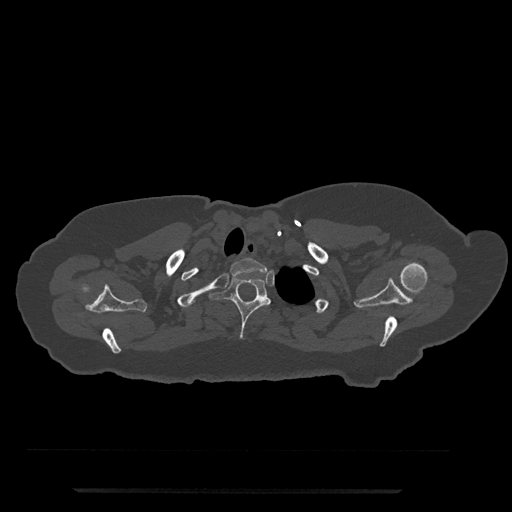
CT including the spine, one axial slice; slice 679 of 797 in the series (ordered by position); reconstruction kernel Br40s/3; bone window (W 1800 / L 400 HU); 0.5 mm slice thickness; 512 × 512 image matrix, field of view 440 × 440 mm. Patient: female, 51 years. From the clinical record (not read from this slice): primary cancer: neuro.
Annotated regions visible in this slice (semi-automatically segmented with operator editing):
- T1 vertebra: bounding box <230,258,267,275> (left, top, right, bottom; pixels)
- T2 vertebra: <210,275,271,339>